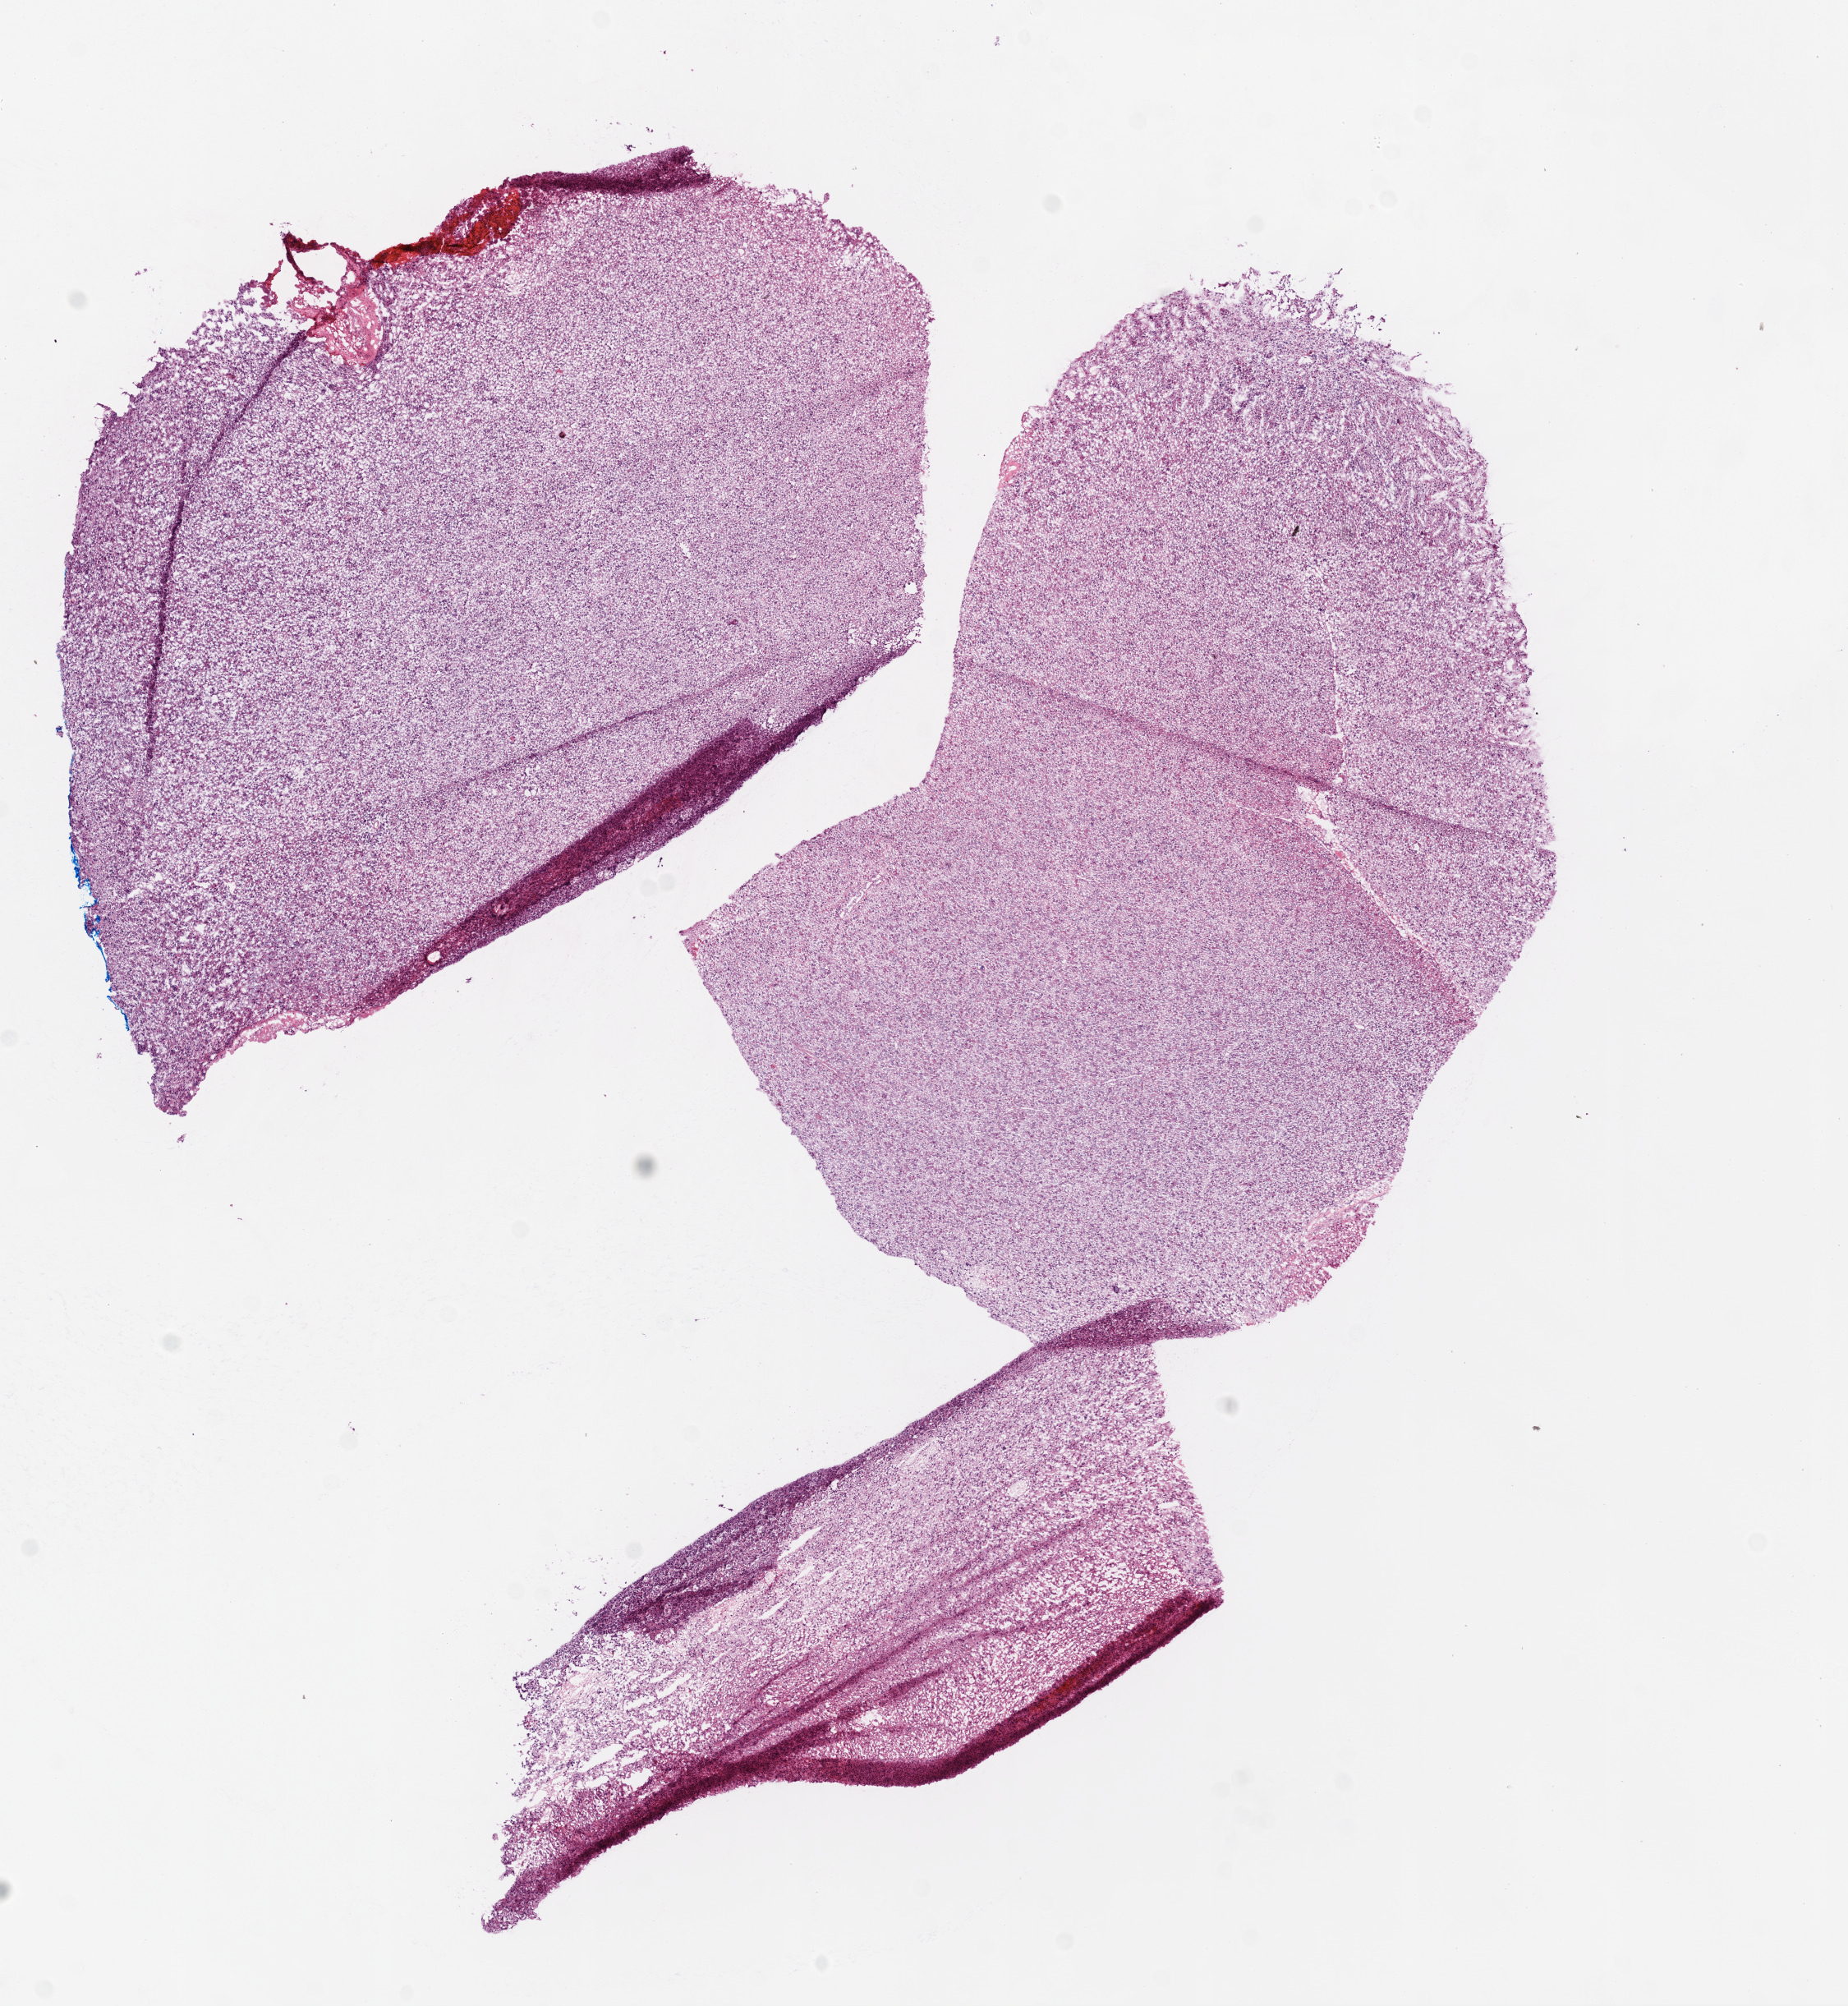
H&E-stained whole-slide image, whole scanned area (about 9.0 x 9.8 mm) shown as a low-resolution overview. Frozen section from the bottom of the tissue portion. Sample: primary tumour, brain. Male, age 59 years at initial diagnosis. Slide review estimates, as recorded: tumour cells 95%, tumour nuclei 85%, normal cells 0%, stromal cells 0%, necrosis 5%.
Diagnosis: Glioblastoma.